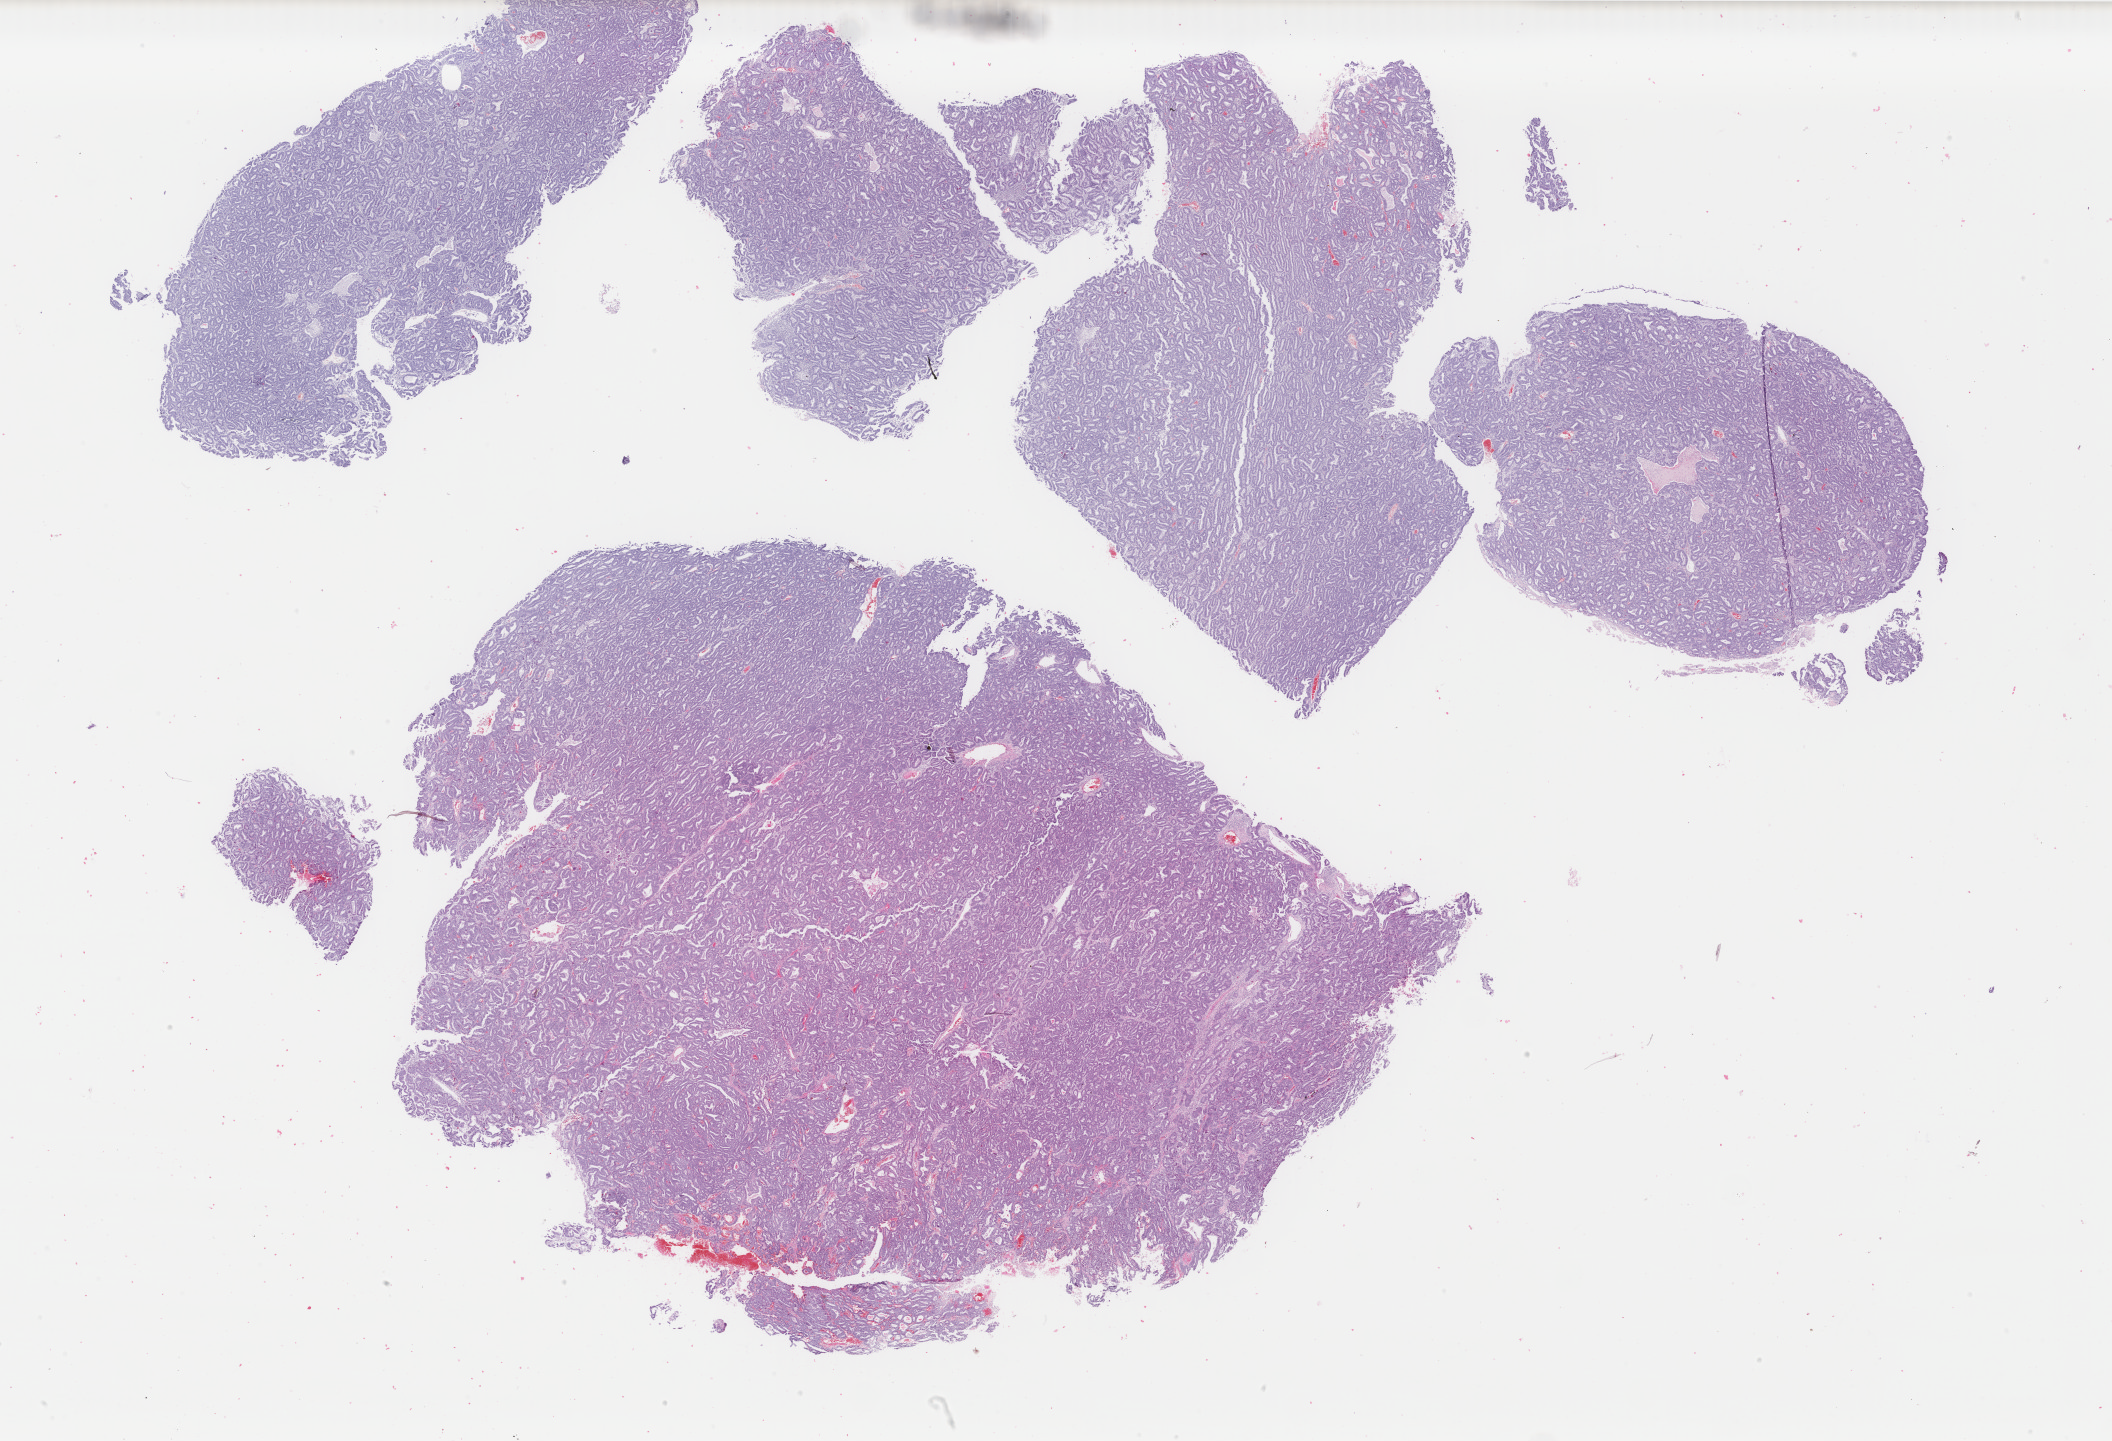
Hematoxylin and eosin (H&E) stained whole-slide image, low-resolution overview of the scanned area, about 33.5 x 22.9 mm, formalin-fixed paraffin-embedded (FFPE) diagnostic section, sample: primary tumour, uterus. Female, age 64 years at initial diagnosis. Histologic grade: G1 (well differentiated).
FIGO stage: IA. Pathologic diagnosis: Endometrioid adenocarcinoma, NOS (endometrium).